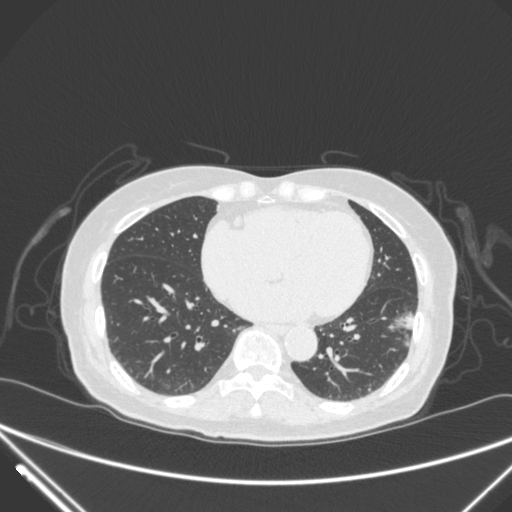
Chest CT, one axial slice. Slice 114 of 310 in the series (ordered by position). Lung window (W 1500 / L -600 HU). 1 mm slice thickness. 512 × 512 image matrix. Female patient, age 82 years. From the clinical record (not read from this slice): clinical TNM (as recorded): T1c N0 M0.
Outlined on this slice (bounding box drawn by a radiologist):
- lung tumour (recorded histology: adenocarcinoma): bounding box (x1, y1, x2, y2) in pixels: (384, 303, 433, 360)